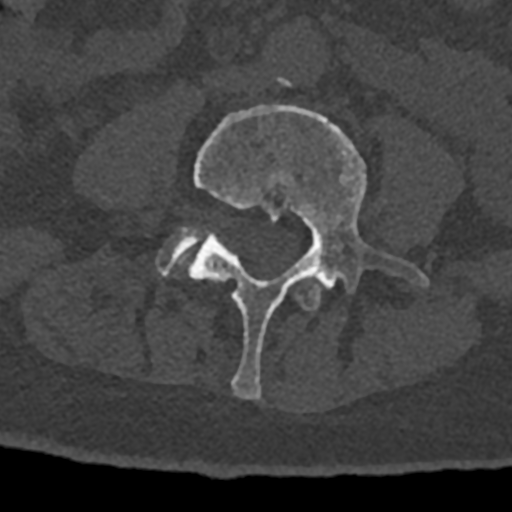
CT including the spine, one axial slice. Slice 257 of 797 in the series (ordered by position). Reconstruction kernel Br40s/3. Bone window (W 1800 / L 400 HU). 0.5 mm slice thickness. 512 × 512 image matrix. Male patient, age 74 years. From the clinical record (not read from this slice): primary cancer: renal; vertebrae with lytic lesions (as recorded): T10, L1, L2, L3, L4, L5.
Structures marked on this image (semi-automatic segmentation, software-assisted and operator-edited):
- L3 vertebra: bounding box [x1, y1, x2, y2] px = [297, 276, 321, 311]
- L4 vertebra: [188, 105, 429, 399]
- L5 vertebra: [158, 227, 199, 276]